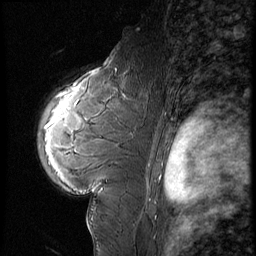
Breast MRI (dynamic contrast-enhanced), one sagittal slice. Slice 43 of 60 in the series (ordered by position). 3 images stored at this slice position (order not interpretable as contrast timing). 1.5 T. TE 4.2 ms, TR 8.9 ms. 256 × 256 image matrix, field of view 200 × 200 mm. Female patient, age 29 years. From the clinical record (not read from this slice): setting: breast cancer imaged before/during neoadjuvant chemotherapy.
Outlined on this slice (semi-automatically segmented with operator editing):
- analysis volume of interest (the breast-tissue region the enhancement analysis was run in; not a lesion): bounding box <39,57,146,200> (left, top, right, bottom; pixels)
- tumour enhancement mask (voxels above the 140 % enhancement threshold inside the analysis volume of interest): <46,89,75,129>